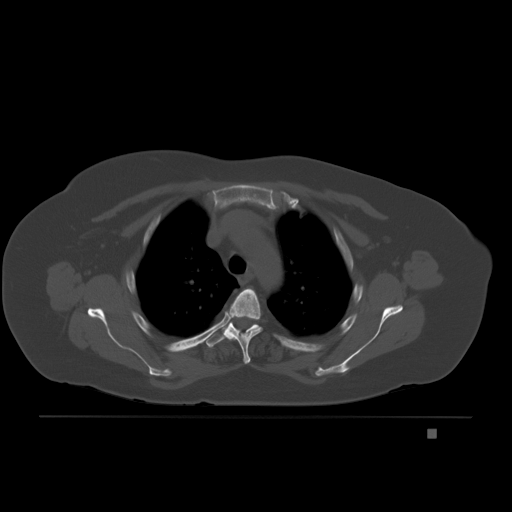
CT including the spine, one axial slice; position 157 of 221 along the scan axis; bone window (W 1800 / L 400 HU); 3 mm slice thickness; 512 × 512 image matrix, field of view 474 × 474 mm. Female patient, age 63 years. From the clinical record (not read from this slice): primary cancer: breast.
Structures marked on this image (semi-automatically segmented with operator editing):
- T3 vertebra: bounding box (x1, y1, x2, y2) in pixels: (223, 289, 263, 364)
- T4 vertebra: (206, 322, 259, 348)